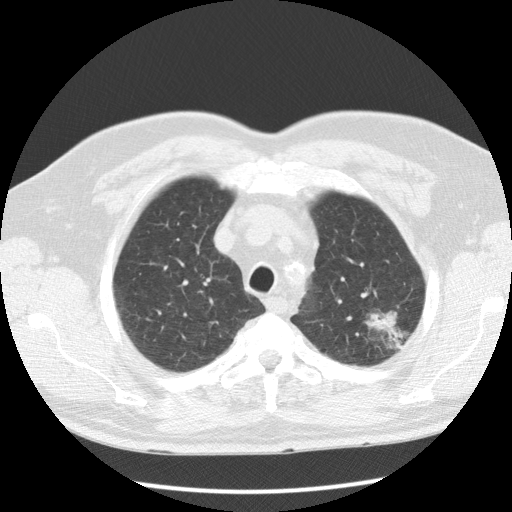
Axial slice from a low-dose chest CT screening exam; baseline screening round; lung window (W 1500 / L -600 HU); 2.5 mm slice thickness; standard (soft-tissue) reconstruction kernel (STANDARD); 120 kVp; slice 23 of 123 in the series; 512 × 512 image matrix. Male participant, aged 60 years at enrolment. Current smoker at enrolment.
• Expert-annotated lung lesion, bounding box [x1, y1, x2, y2] px = [357, 298, 416, 360].
• The screening reader recorded 3 non-calcified nodules or masses ≥4 mm on this exam (left upper lobe, right upper lobe, left upper lobe); which of them this box marks is not recorded.
• Official screen result: positive, change unspecified: nodule(s) >= 4 mm or enlarging nodule(s), mass(es), or other non-specific abnormalities suspicious for lung cancer.
• Lung cancer was diagnosed 48 days after this screen: bronchiolo-alveolar adenocarcinoma, NOS, left upper lobe, well differentiated (G1), stage IA (AJCC 6th edition), 27 mm at pathology.